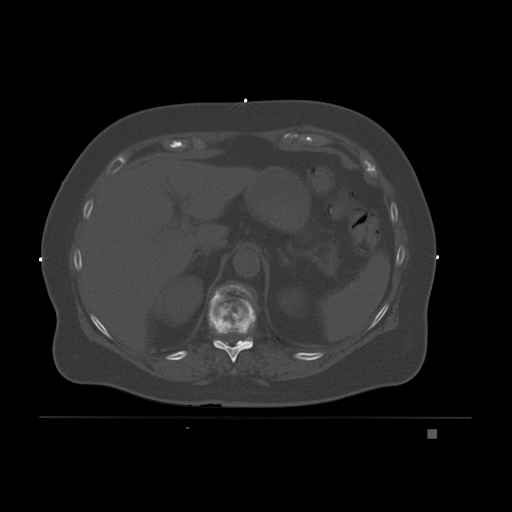
CT including the spine, one axial slice; position 97 of 221 along the scan axis; bone window (W 1800 / L 400 HU); 3 mm slice thickness; 512 × 512 image matrix, field of view 474 × 474 mm. Patient: female, 63 years. From the clinical record (not read from this slice): primary cancer: breast.
Structures marked on this image (semi-automatic segmentation, software-assisted and operator-edited):
- T10 vertebra: bounding box <208,294,256,363> (left, top, right, bottom; pixels)
- T11 vertebra: <212,284,253,346>